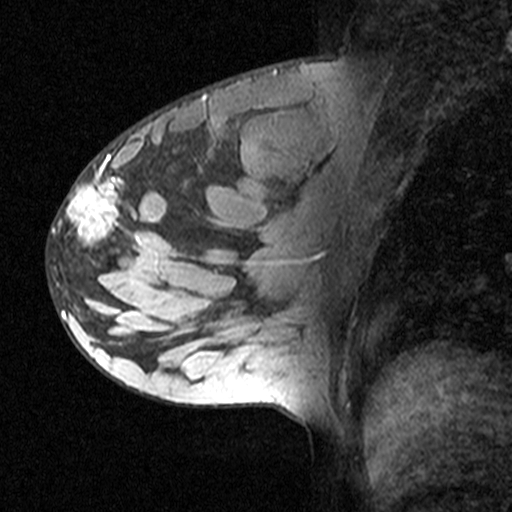
Breast MRI (dynamic contrast-enhanced), one sagittal slice; position 20 of 44 along the scan axis; dynamic contrast-enhanced study with each time point stored as its own series, time point 2 of 3 at this slice position (early post-contrast, ordered by acquisition time); 1.5 T; TE 4.5 ms, TR 11 ms; 3 mm slice thickness; 512 × 512 image matrix, field of view 200 × 200 mm. Patient: female, 27 years. Case-level facts recorded for this patient, not image findings: setting: breast cancer imaged before/during neoadjuvant chemotherapy; receptor status: HR-positive, HER2-negative.
Structures marked on this image (semi-automatically segmented with operator editing):
- analysis volume of interest (the breast-tissue region the enhancement analysis was run in; not a lesion): bounding box (x1, y1, x2, y2) in pixels: (47, 162, 163, 271)
- tumour enhancement mask (voxels above the 90 % enhancement threshold inside the analysis volume of interest): (53, 162, 123, 247)